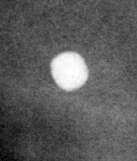
Cropped region of a digitized screen-film mammogram centred on a radiologist-marked abnormality, left breast, CC view.
Calcifications, morphology round and regular / lucent center / punctate, distribution diffusely scattered; BI-RADS assessment category 2; subtlety rating 5 on a 1 (subtle) to 5 (obvious) scale; benign; no additional work-up was recommended (benign without callback).